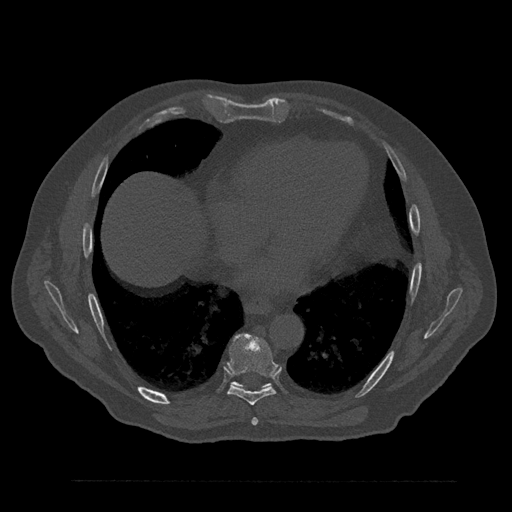
CT including the spine, one axial slice; position 446 of 797 along the scan axis; 120 kVp; bone window (W 1800 / L 400 HU); 0.5 mm slice thickness; 512 × 512 image matrix, field of view 430 × 430 mm. Male patient, age 61 years. Case-level facts recorded for this patient, not image findings: primary cancer: prostate.
Annotated regions visible in this slice (semi-automatically segmented with operator editing):
- T7 vertebra: bounding box <252,418,258,425> (left, top, right, bottom; pixels)
- T8 vertebra: <228,334,278,405>
- T9 vertebra: <232,381,271,387>